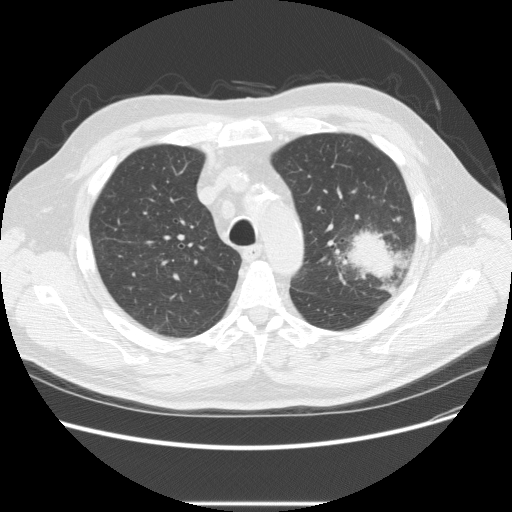
Chest CT (low-dose screening protocol), one axial image. Baseline screening round. Lung window (W 1500 / L -600 HU). 2.5 mm slice thickness. Standard (soft-tissue) reconstruction kernel (STANDARD). 512 × 512 image matrix. Male, age 73 years at enrolment. Former smoker at enrolment.
Lesion marked by an expert reader, box from (x=332, y=215) to (x=417, y=286) px. The screening reader recorded 2 non-calcified nodules or masses ≥4 mm on this exam (left upper lobe, right upper lobe); which of them this box marks is not recorded. Official screen result: positive, change unspecified: nodule(s) >= 4 mm or enlarging nodule(s), mass(es), or other non-specific abnormalities suspicious for lung cancer. Lung cancer was diagnosed 11 days after this screen: bronchiolo-alveolar adenocarcinoma, NOS, other location, well differentiated (G1), stage IV (AJCC 6th edition).